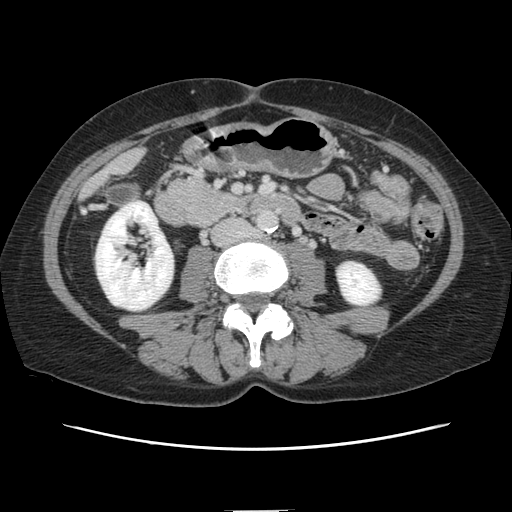
Contrast-enhanced abdominal CT, one axial slice; position 26 of 141 along the scan axis; intravenous contrast given; soft-tissue window (W 400 / L 40 HU); 2.5 mm slice thickness; 512 × 512 image matrix, field of view 350 × 350 mm. Female patient, age 63 years. From the clinical record (not read from this slice): diagnosis: colorectal cancer liver metastases, imaged before liver resection; multiple liver metastases: yes; largest metastasis: 3.2 cm; disease in both lobes: yes.
Structures marked on this image (outlined manually by an expert reader):
- liver: bounding box [x1, y1, x2, y2] px = [85, 151, 141, 194]